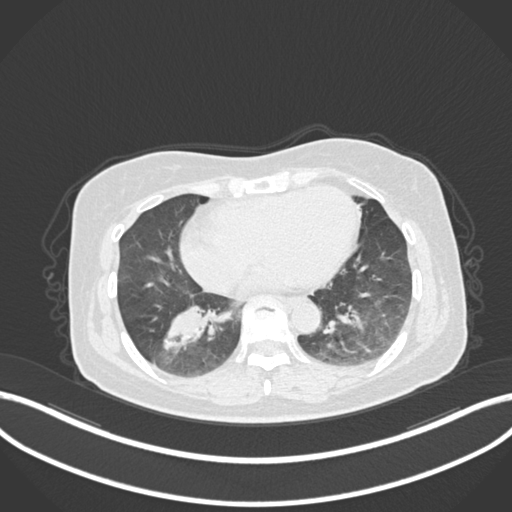
Chest CT, one axial slice; position 49 of 222 along the scan axis; 120 kVp; lung window (W 1500 / L -600 HU); 1 mm slice thickness; 512 × 512 image matrix, field of view 400 × 400 mm. Patient: female, 67 years. From the clinical record (not read from this slice): clinical TNM (as recorded): T1c N1 M0; histopathological grade: G2-3.
Outlined on this slice (rectangle marked by the reading radiologist):
- lung tumour (recorded histology: adenocarcinoma): bounding box [x1, y1, x2, y2] px = [155, 301, 211, 356]